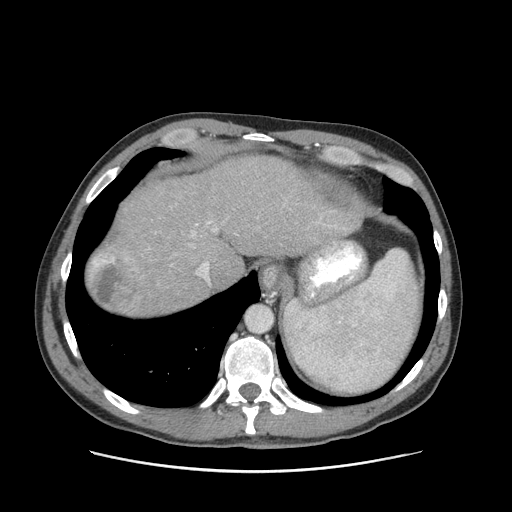
Contrast-enhanced abdominal CT (liver protocol), one axial slice; slice 79 of 93 in the series (ordered by position); 120 kVp; soft-tissue window (W 400 / L 40 HU); 2.5 mm slice thickness; 512 × 512 image matrix, field of view 380 × 380 mm. Case-level facts recorded for this patient, not image findings: diagnosis: hepatocellular carcinoma (patient treated with transarterial chemoembolisation; whether this scan precedes or follows treatment is not stated here); TNM stage (as recorded): Stage-II; Child-Pugh class: A; tumour differentiation: moderately differentiated; tumour nodularity: multinodular.
Structures marked on this image (semi-automatically segmented with operator editing):
- abdominal aorta: bounding box [x1, y1, x2, y2] px = [245, 305, 272, 331]
- liver parenchyma outside the tumour (the mass and vessels are separate outlines, so this box may not span the whole liver): [88, 156, 362, 316]
- mass: [91, 248, 142, 311]
- liver vessels: [196, 221, 217, 281]